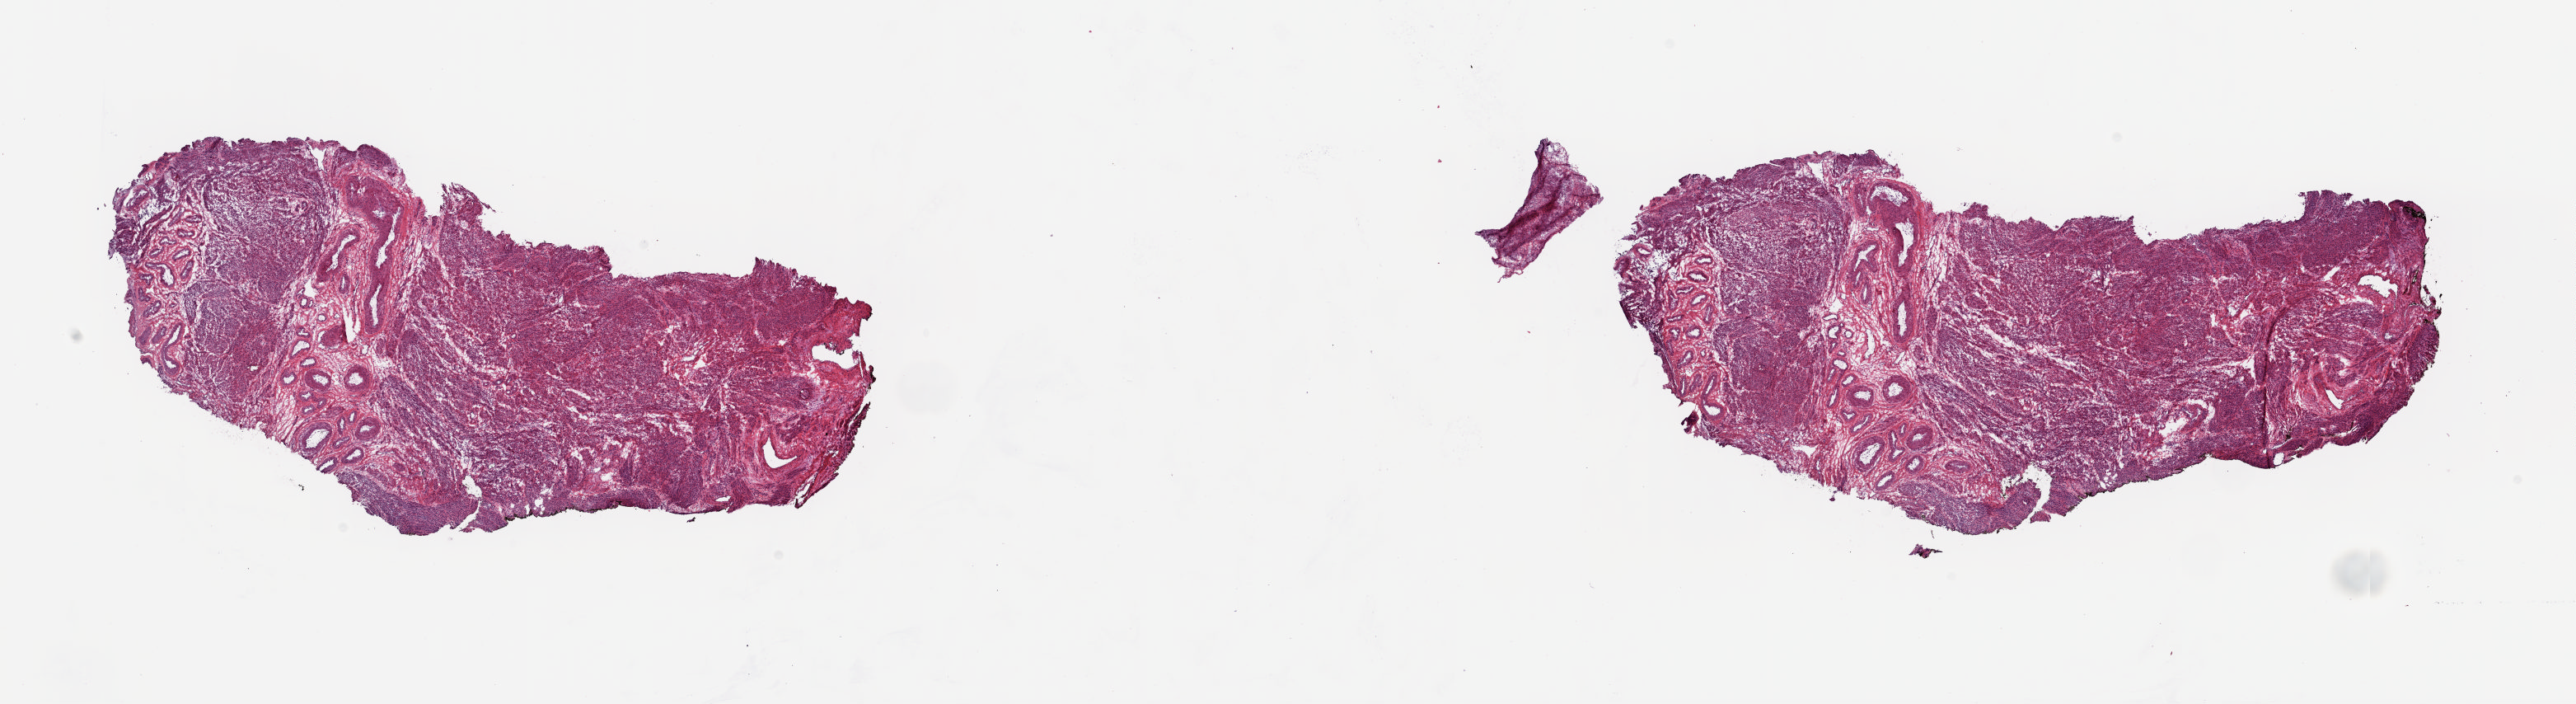
Hematoxylin and eosin (H&E) stained whole-slide image — whole scanned area (about 24.8 x 6.8 mm, acquisition: 20x scan) shown as a low-resolution overview, frozen section from the top of the tissue portion, sample: solid tissue normal (non-tumour tissue), uterus. Female, age 63 years at initial diagnosis. Pathologist review of this section (percent, as recorded): tumour cells 0%, tumour nuclei 0%, normal cells 100%, stromal cells 0%, necrosis 0%. Inflammatory infiltration, as recorded: lymphocyte infiltration 1%, monocyte infiltration 0%, neutrophil infiltration 0%.
This section: solid tissue normal (non-tumour) sample from the same patient. Patient diagnosis: Endometrioid adenocarcinoma, NOS (endometrium).